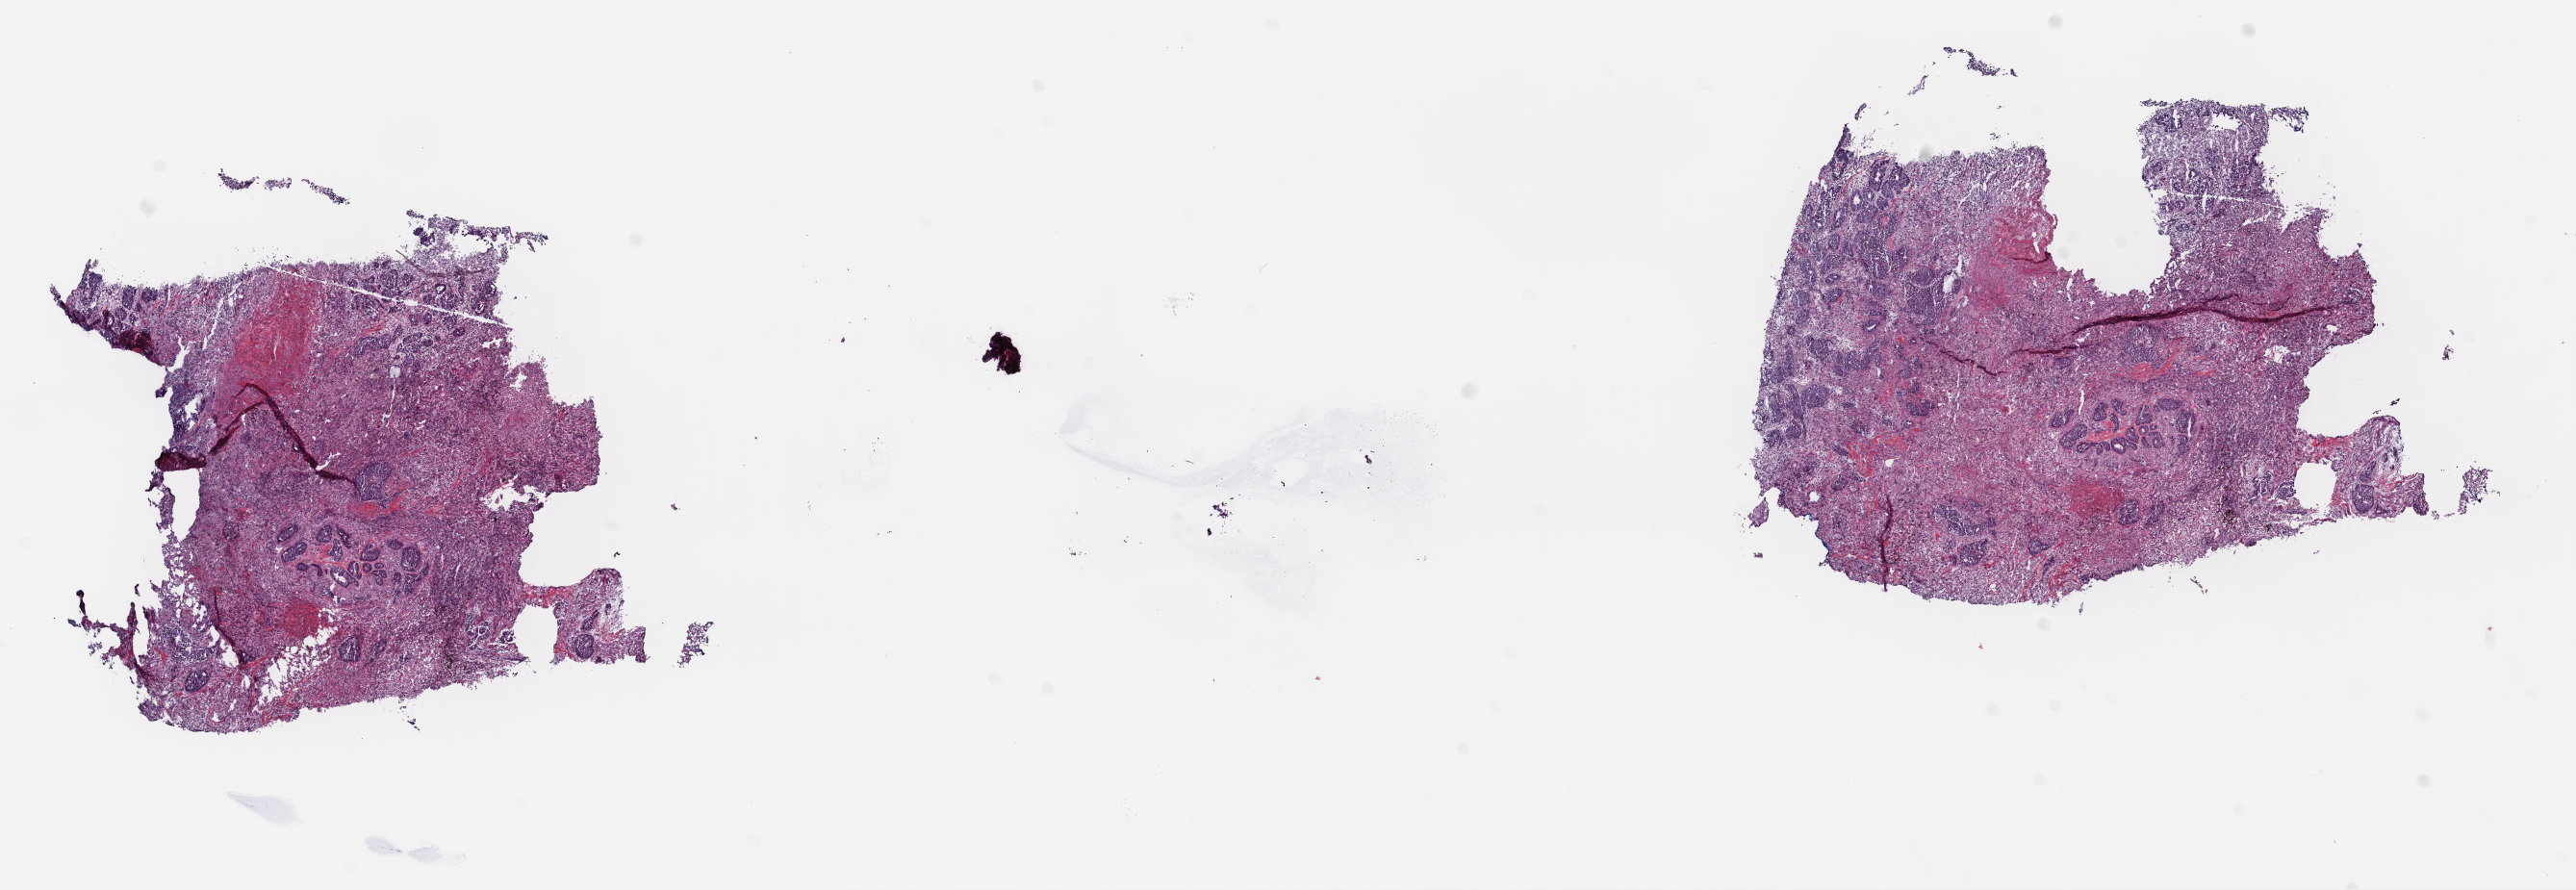
Digitized H&E-stained tissue section (whole slide) — low-resolution overview of the scanned area, about 21.0 x 7.3 mm; frozen section from the top of the tissue portion; primary tumour sample from the lung. Patient: male, age at initial diagnosis 67 years. Composition of this section per pathologist review: tumour cells 25%, tumour nuclei 100%, normal cells 0%, stromal cells 75%, necrosis 0%. Inflammatory infiltration, as recorded: lymphocyte infiltration 3%, monocyte infiltration 4%, neutrophil infiltration 1%.
Pathologic diagnosis: Solid carcinoma, NOS (upper lobe, lung). AJCC pathologic stage: IA (7th edition).